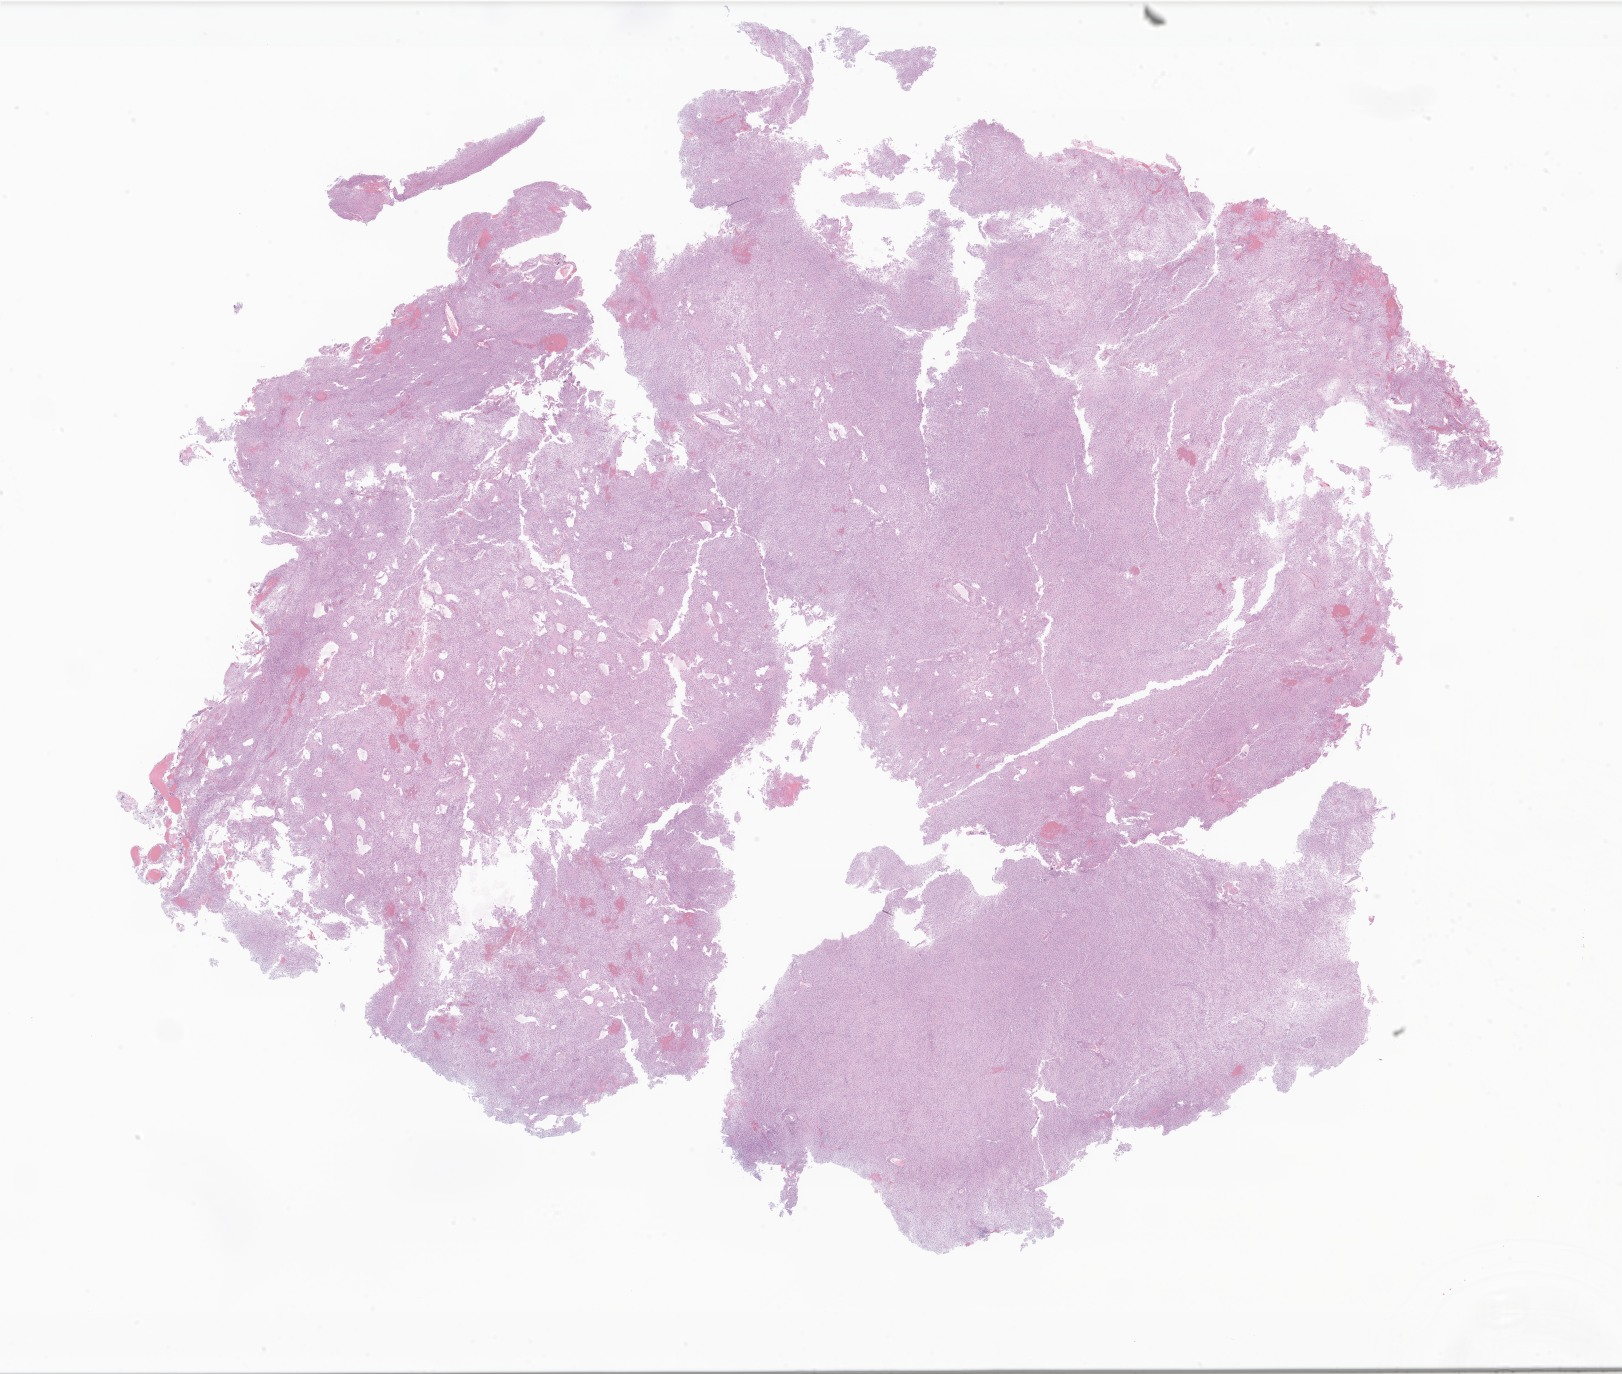
Digitized haematoxylin and eosin-stained section of tumor tissue from the brain — shown as a low-resolution overview of the whole scanned area (about 27.4 x 23.2 mm). Formalin-fixed, paraffin-embedded (FFPE) tissue. Female patient, age 56 months.
Diagnosis (ICD-O-3 morphology term): Pilocytic astrocytoma.